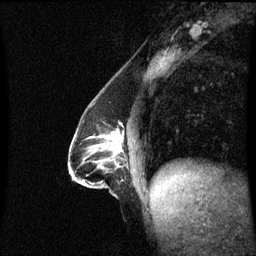
Breast MRI (dynamic contrast-enhanced), one sagittal slice. Position 29 of 60 along the scan axis. Dynamic contrast-enhanced series, image 2 of 3 at this slice position (ordered by acquisition). 1.5 T. TE 4.2 ms, TR 8.9 ms. 2.2 mm slice thickness. 256 × 256 image matrix, field of view 210 × 210 mm. Patient: female, 47 years. Case-level facts recorded for this patient, not image findings: setting: breast cancer imaged before/during neoadjuvant chemotherapy; receptor status: HR-positive, HER2-negative.
Outlined on this slice (semi-automatically segmented with operator editing):
- analysis volume of interest (the breast-tissue region the enhancement analysis was run in; not a lesion): box from (x=70, y=130) to (x=124, y=196) px
- tumour enhancement mask (voxels above the 70 % enhancement threshold inside the analysis volume of interest): (x=114, y=133)–(x=122, y=153)